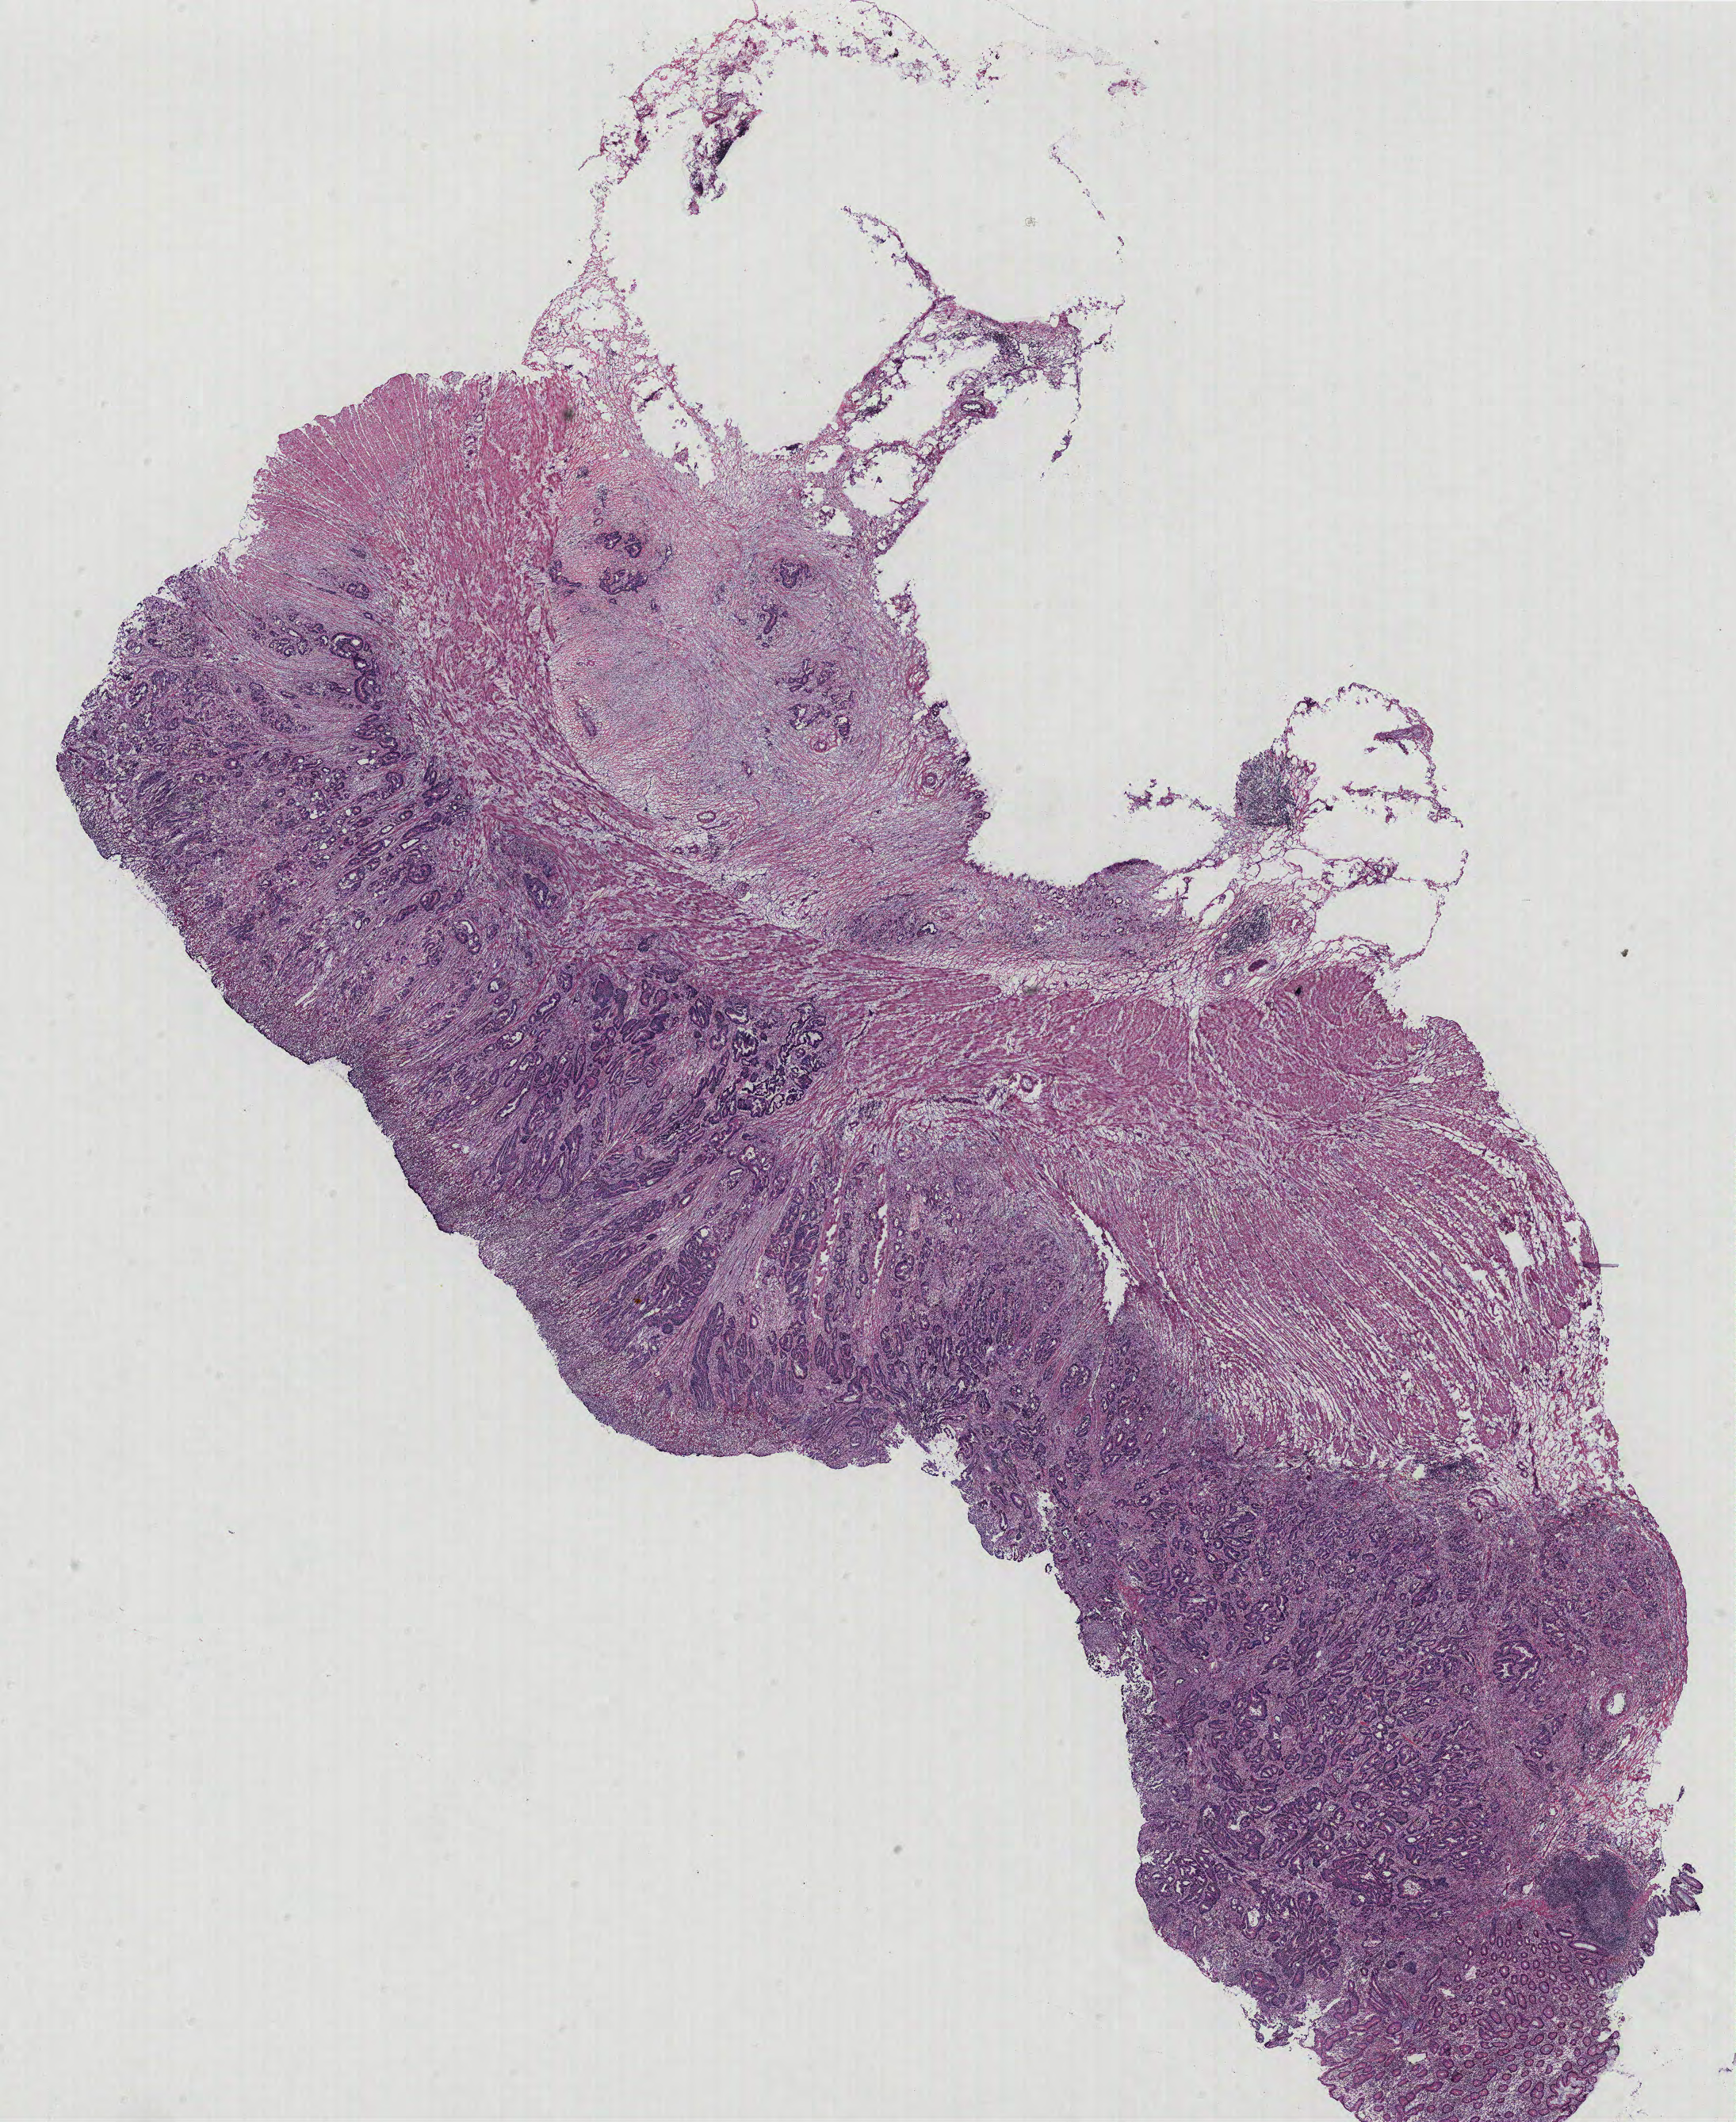
Hematoxylin and eosin (H&E) stained whole-slide image, low-resolution overview of the scanned area, about 17.5 x 21.4 mm (from a 40x scan), tumour tissue sample, colon. Female, 71 y/o.
Histologic diagnosis: Adenocarcinoma, NOS. AJCC pathologic stage: IIIB. Primary tumour site (as recorded): colon.